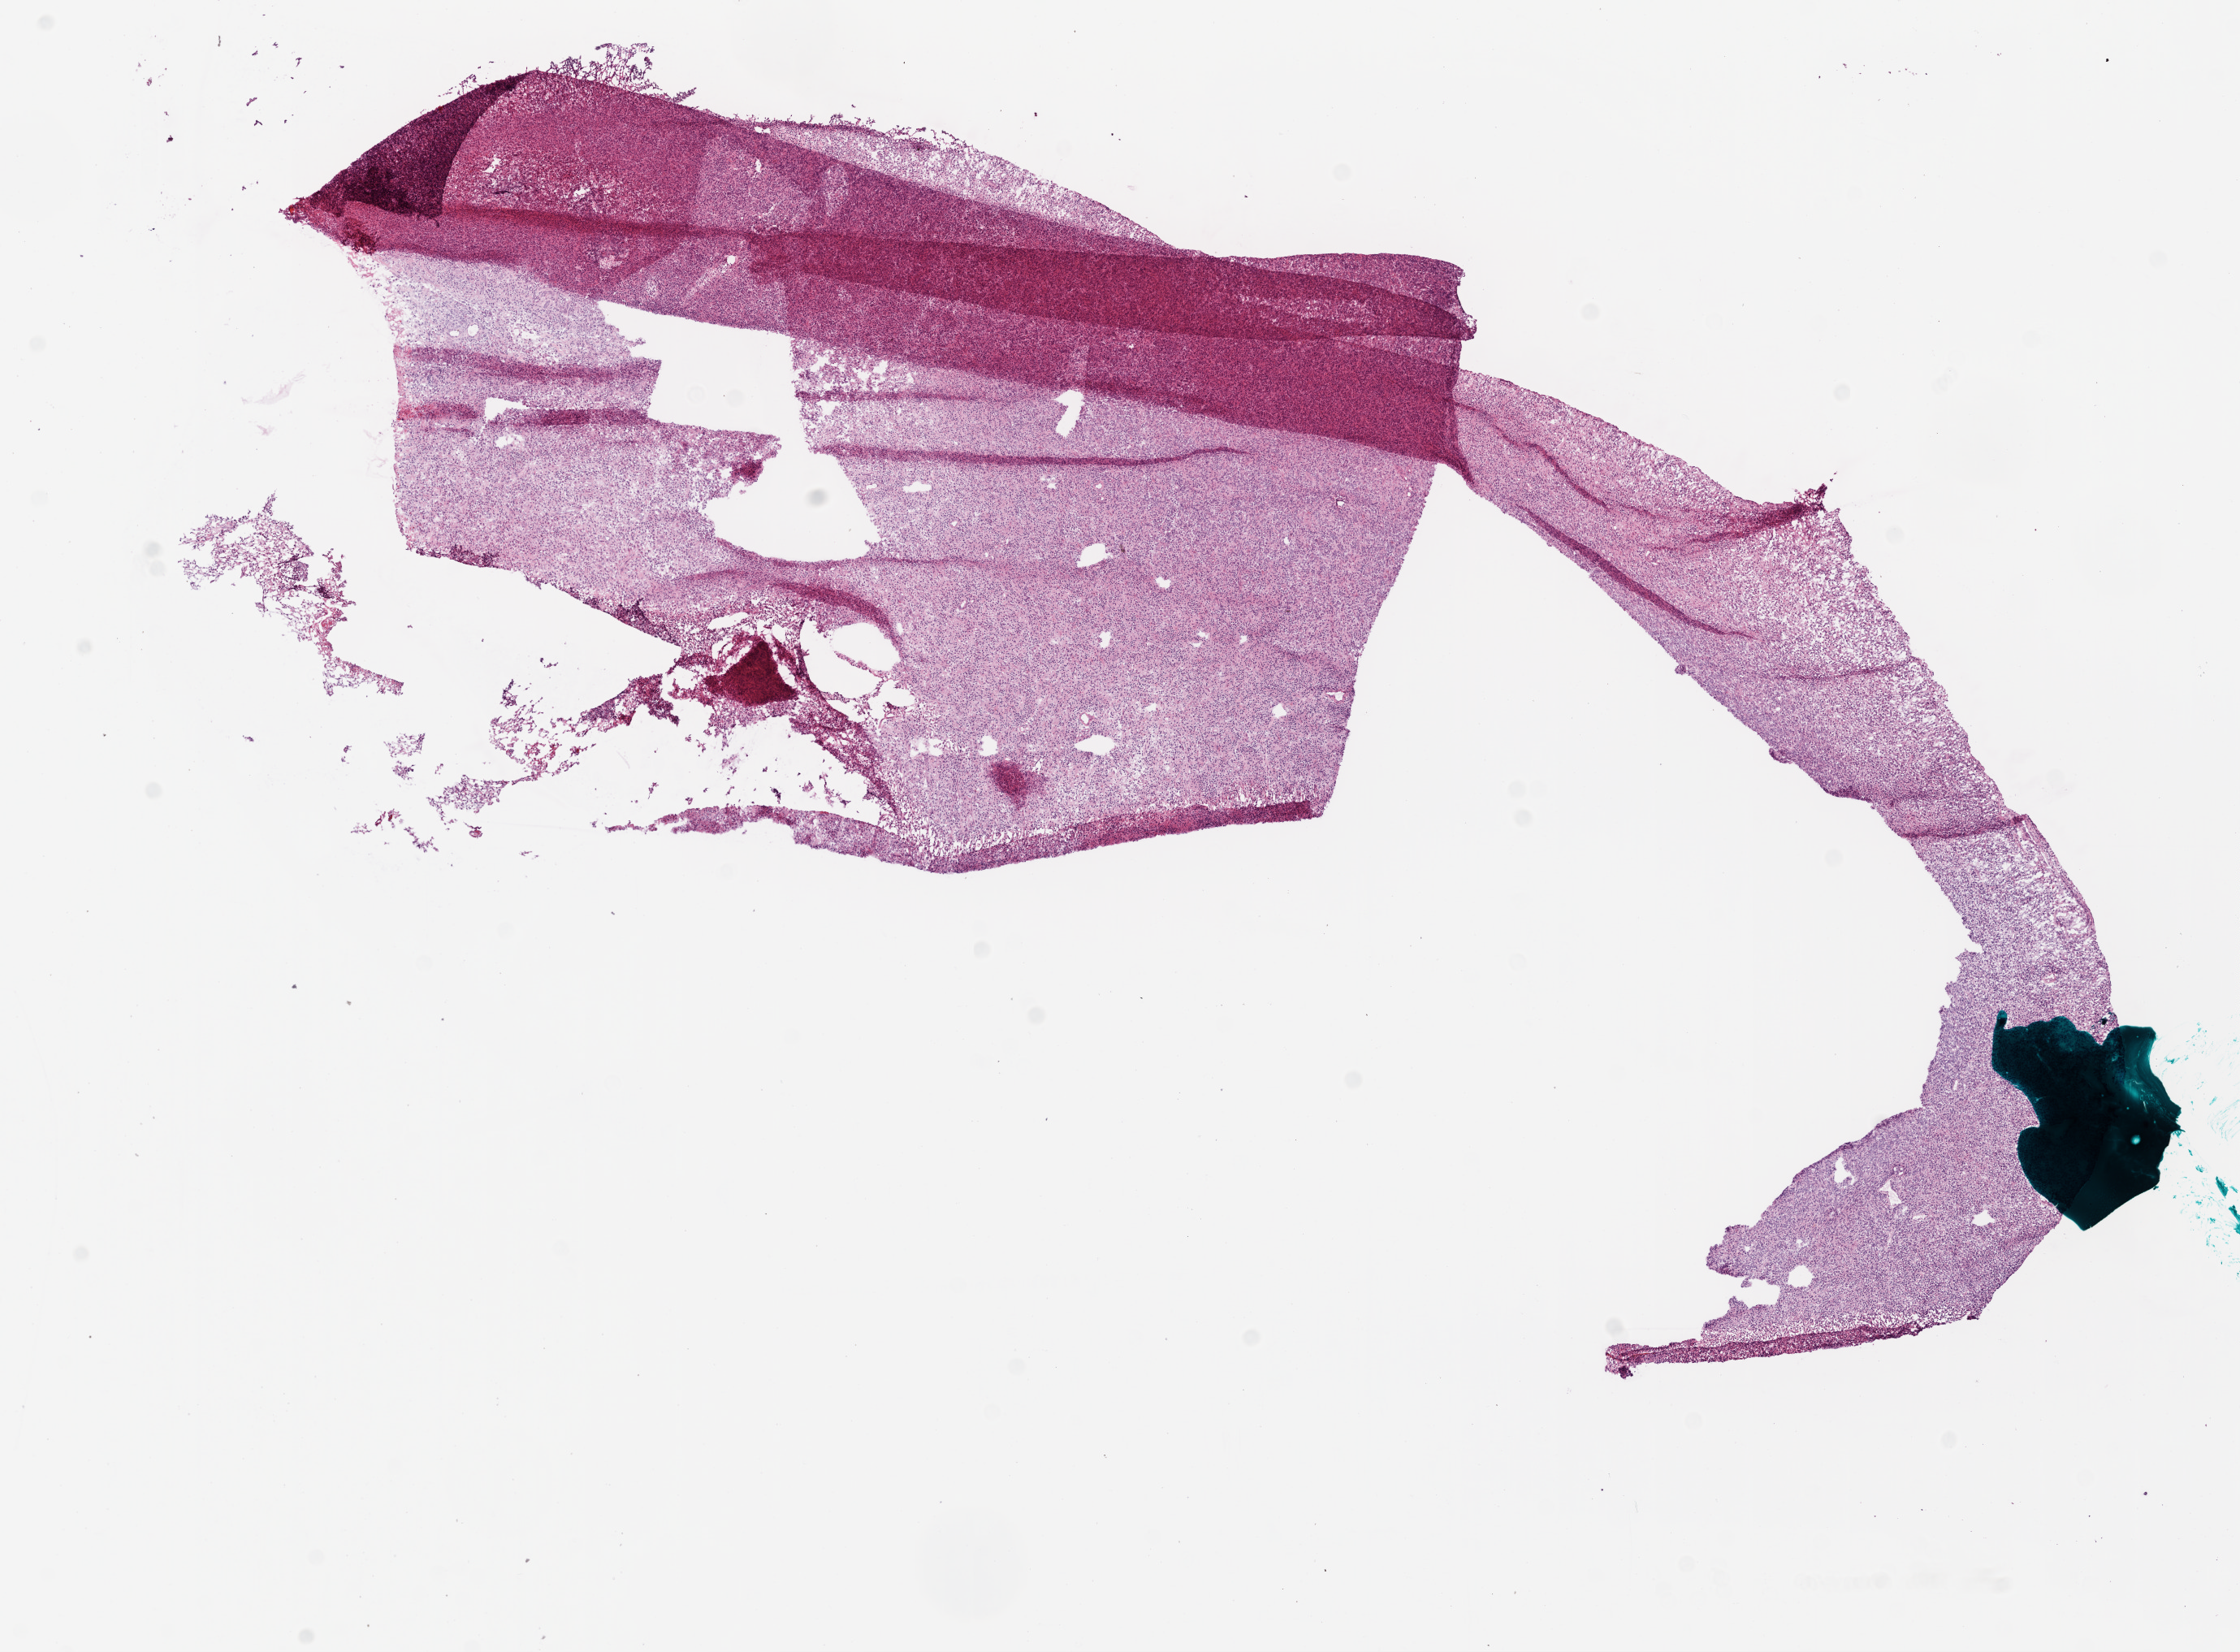
Whole-slide histology image, H&E-stained, whole scanned area (about 11.1 x 8.2 mm) shown as a low-resolution overview; frozen section from the bottom of the tissue portion; sample: primary tumour, brain. Male, age 69 years at initial diagnosis. Slide review estimates, as recorded: tumour cells 100%, tumour nuclei 100%, normal cells 0%, stromal cells 0%, necrosis 0%.
Histologic diagnosis: Glioblastoma.